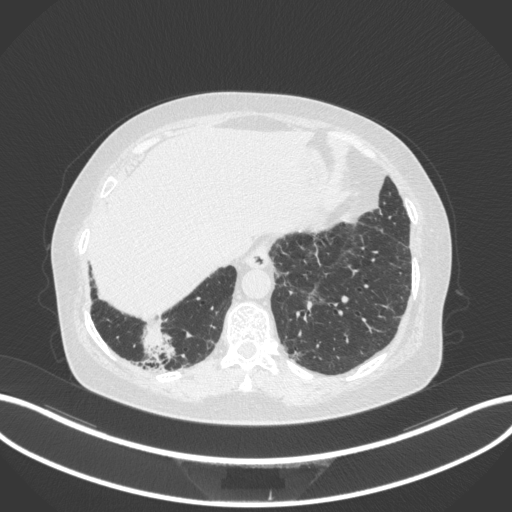
Chest CT, one axial slice; slice 25 of 303 in the series (ordered by position); 120 kVp; lung window (W 1500 / L -600 HU); 1 mm slice thickness; 512 × 512 image matrix. Female patient, age 65 years. From the clinical record (not read from this slice): clinical TNM (as recorded): T2b N1 M0.
Structures marked on this image (bounding box drawn by a radiologist):
- lung tumour (recorded histology: adenocarcinoma): bounding box <138,322,176,365> (left, top, right, bottom; pixels)